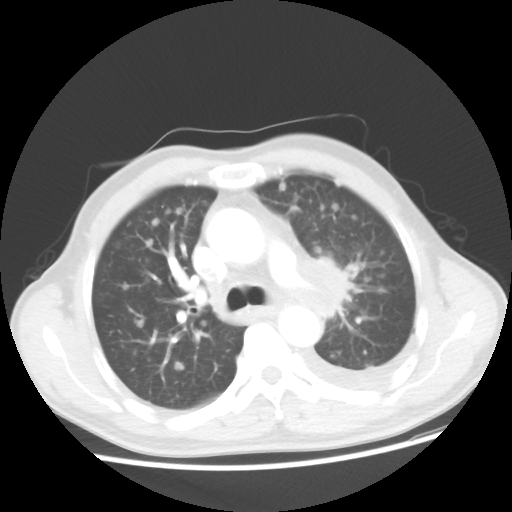
Chest CT, one axial slice; slice 31 of 48 in the series (ordered by position); 100 kVp; lung window (W 1500 / L -600 HU); 5 mm slice thickness; 512 × 512 image matrix, field of view 362 × 362 mm. Male patient, age 55 years. From the clinical record (not read from this slice): clinical TNM (as recorded): T2 N3 M1a.
Outlined on this slice (bounding box drawn by a radiologist):
- lung tumour (recorded histology: squamous cell carcinoma): box from (x=301, y=251) to (x=351, y=323) px